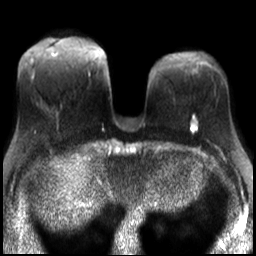
Breast MRI, one axial slice. Slice 11 of 30 in the series (ordered by position). Diffusion-weighted series; image 2 of 4 stored at this slice position (different b-values; order by instance number). 3 T. 4 mm slice thickness. 256 × 256 image matrix, field of view 320 × 320 mm. Female patient.
Outlined on this slice (outlined manually by an expert reader):
- tumour on diffusion-weighted imaging: bounding box <191,119,196,129> (left, top, right, bottom; pixels)